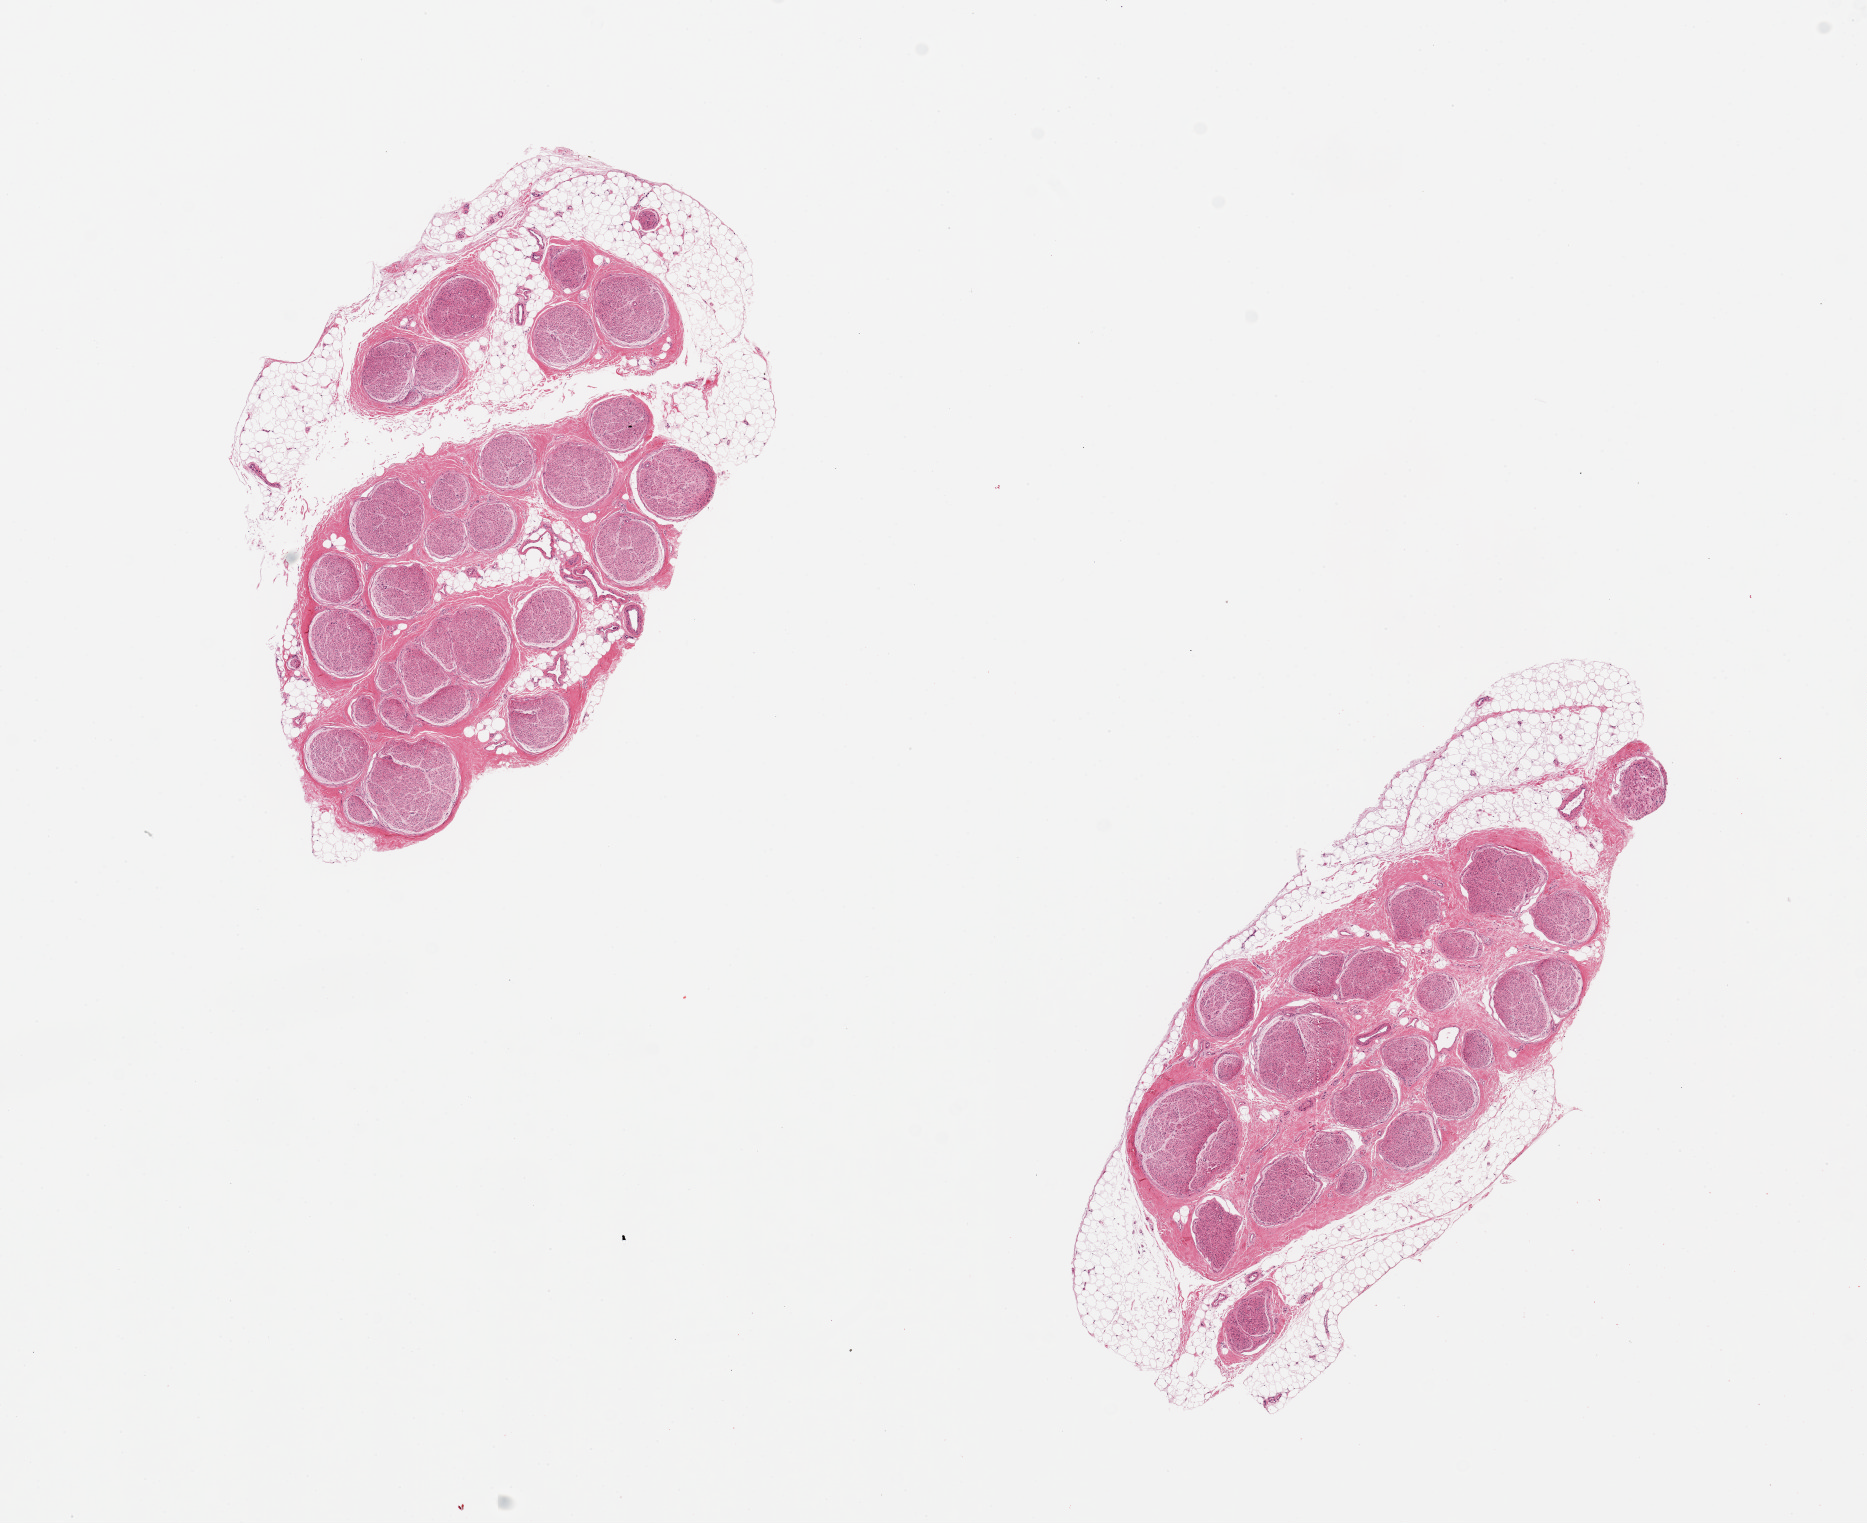
Whole-slide image, hematoxylin and eosin (H&E) stain, low-resolution overview of the scanned area, about 14.8 x 12.0 mm; PAXgene-fixed paraffin-embedded (PFPE) section; section of tibial nerve (target tissue); donor tissue sample. Male donor.
Reviewer comment on this tissue sample: 2 pieces, 6x4 & 7x3mm; 20% peripheral adipose.